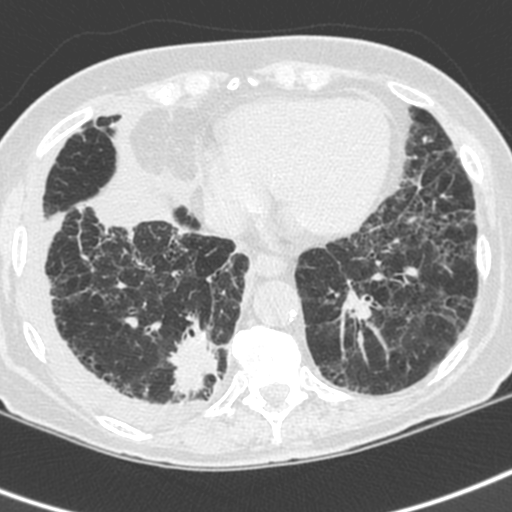
Chest CT (low-dose screening protocol), one axial image, baseline annual screen, lung window (W 1500 / L -600 HU), 1.3 mm slice thickness. Female, age 73 years at enrolment. Current smoker at enrolment.
Expert-annotated lung lesion, bounding box (x1, y1, x2, y2) in pixels: (155, 317, 234, 406). Reader record for this screening exam (exam-level; its link to the box is not recorded): non-calcified nodule or mass ≥4 mm, right lower lobe, 35 × 30 mm, spiculated (stellate) margins, soft tissue attenuation.